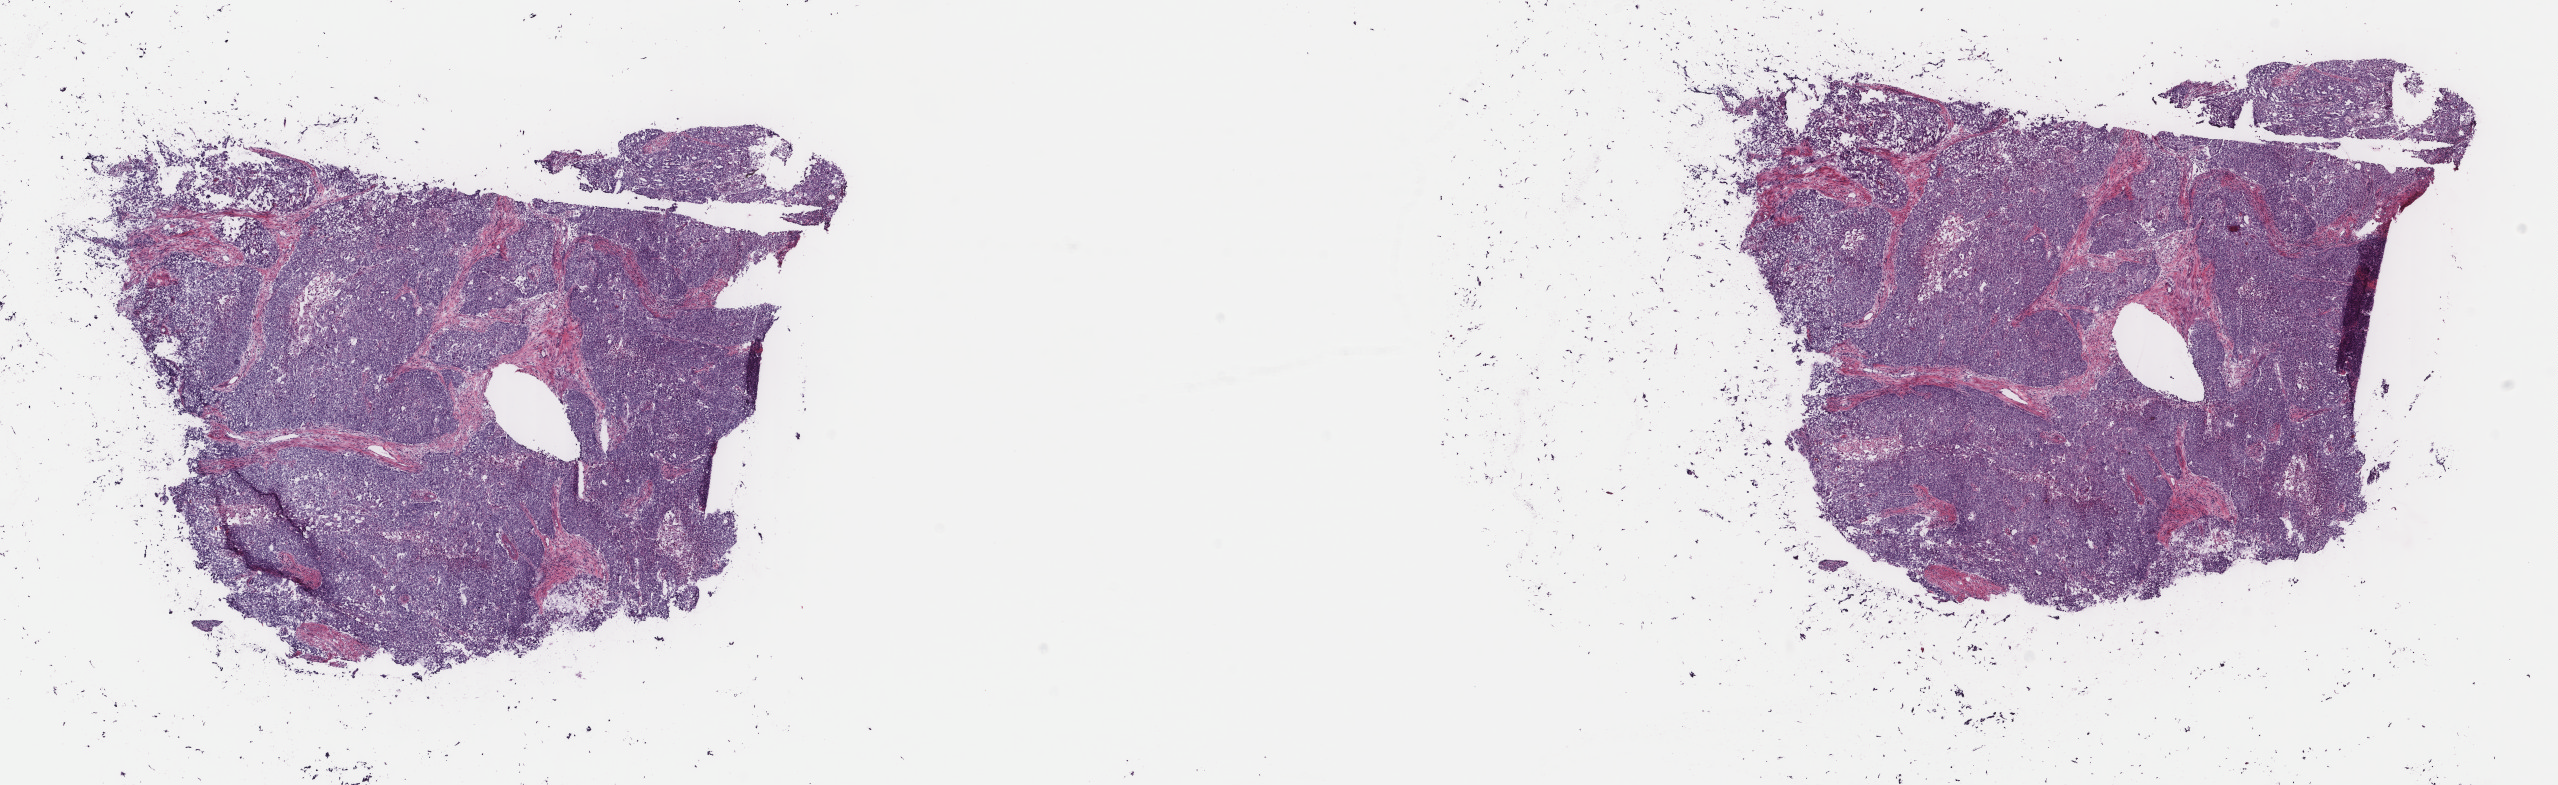
Whole-slide histology image, H&E-stained — shown as a low-resolution overview of the whole scanned area (about 20.3 x 6.2 mm, from a 40x scan). Frozen section from the top of the tissue portion. Primary tumour sample from the uterus. Female, age 60 years at initial diagnosis. Histologic grade: G3 (poorly differentiated). Composition of this section per pathologist review: tumour cells 75%, tumour nuclei 80%, normal cells 0%, stromal cells 20%, necrosis 5%. Inflammatory infiltration, as recorded: lymphocyte infiltration 5%, monocyte infiltration 5%, neutrophil infiltration 10%.
FIGO stage: IIIC. Pathologic diagnosis: Endometrioid adenocarcinoma, NOS (endometrium).